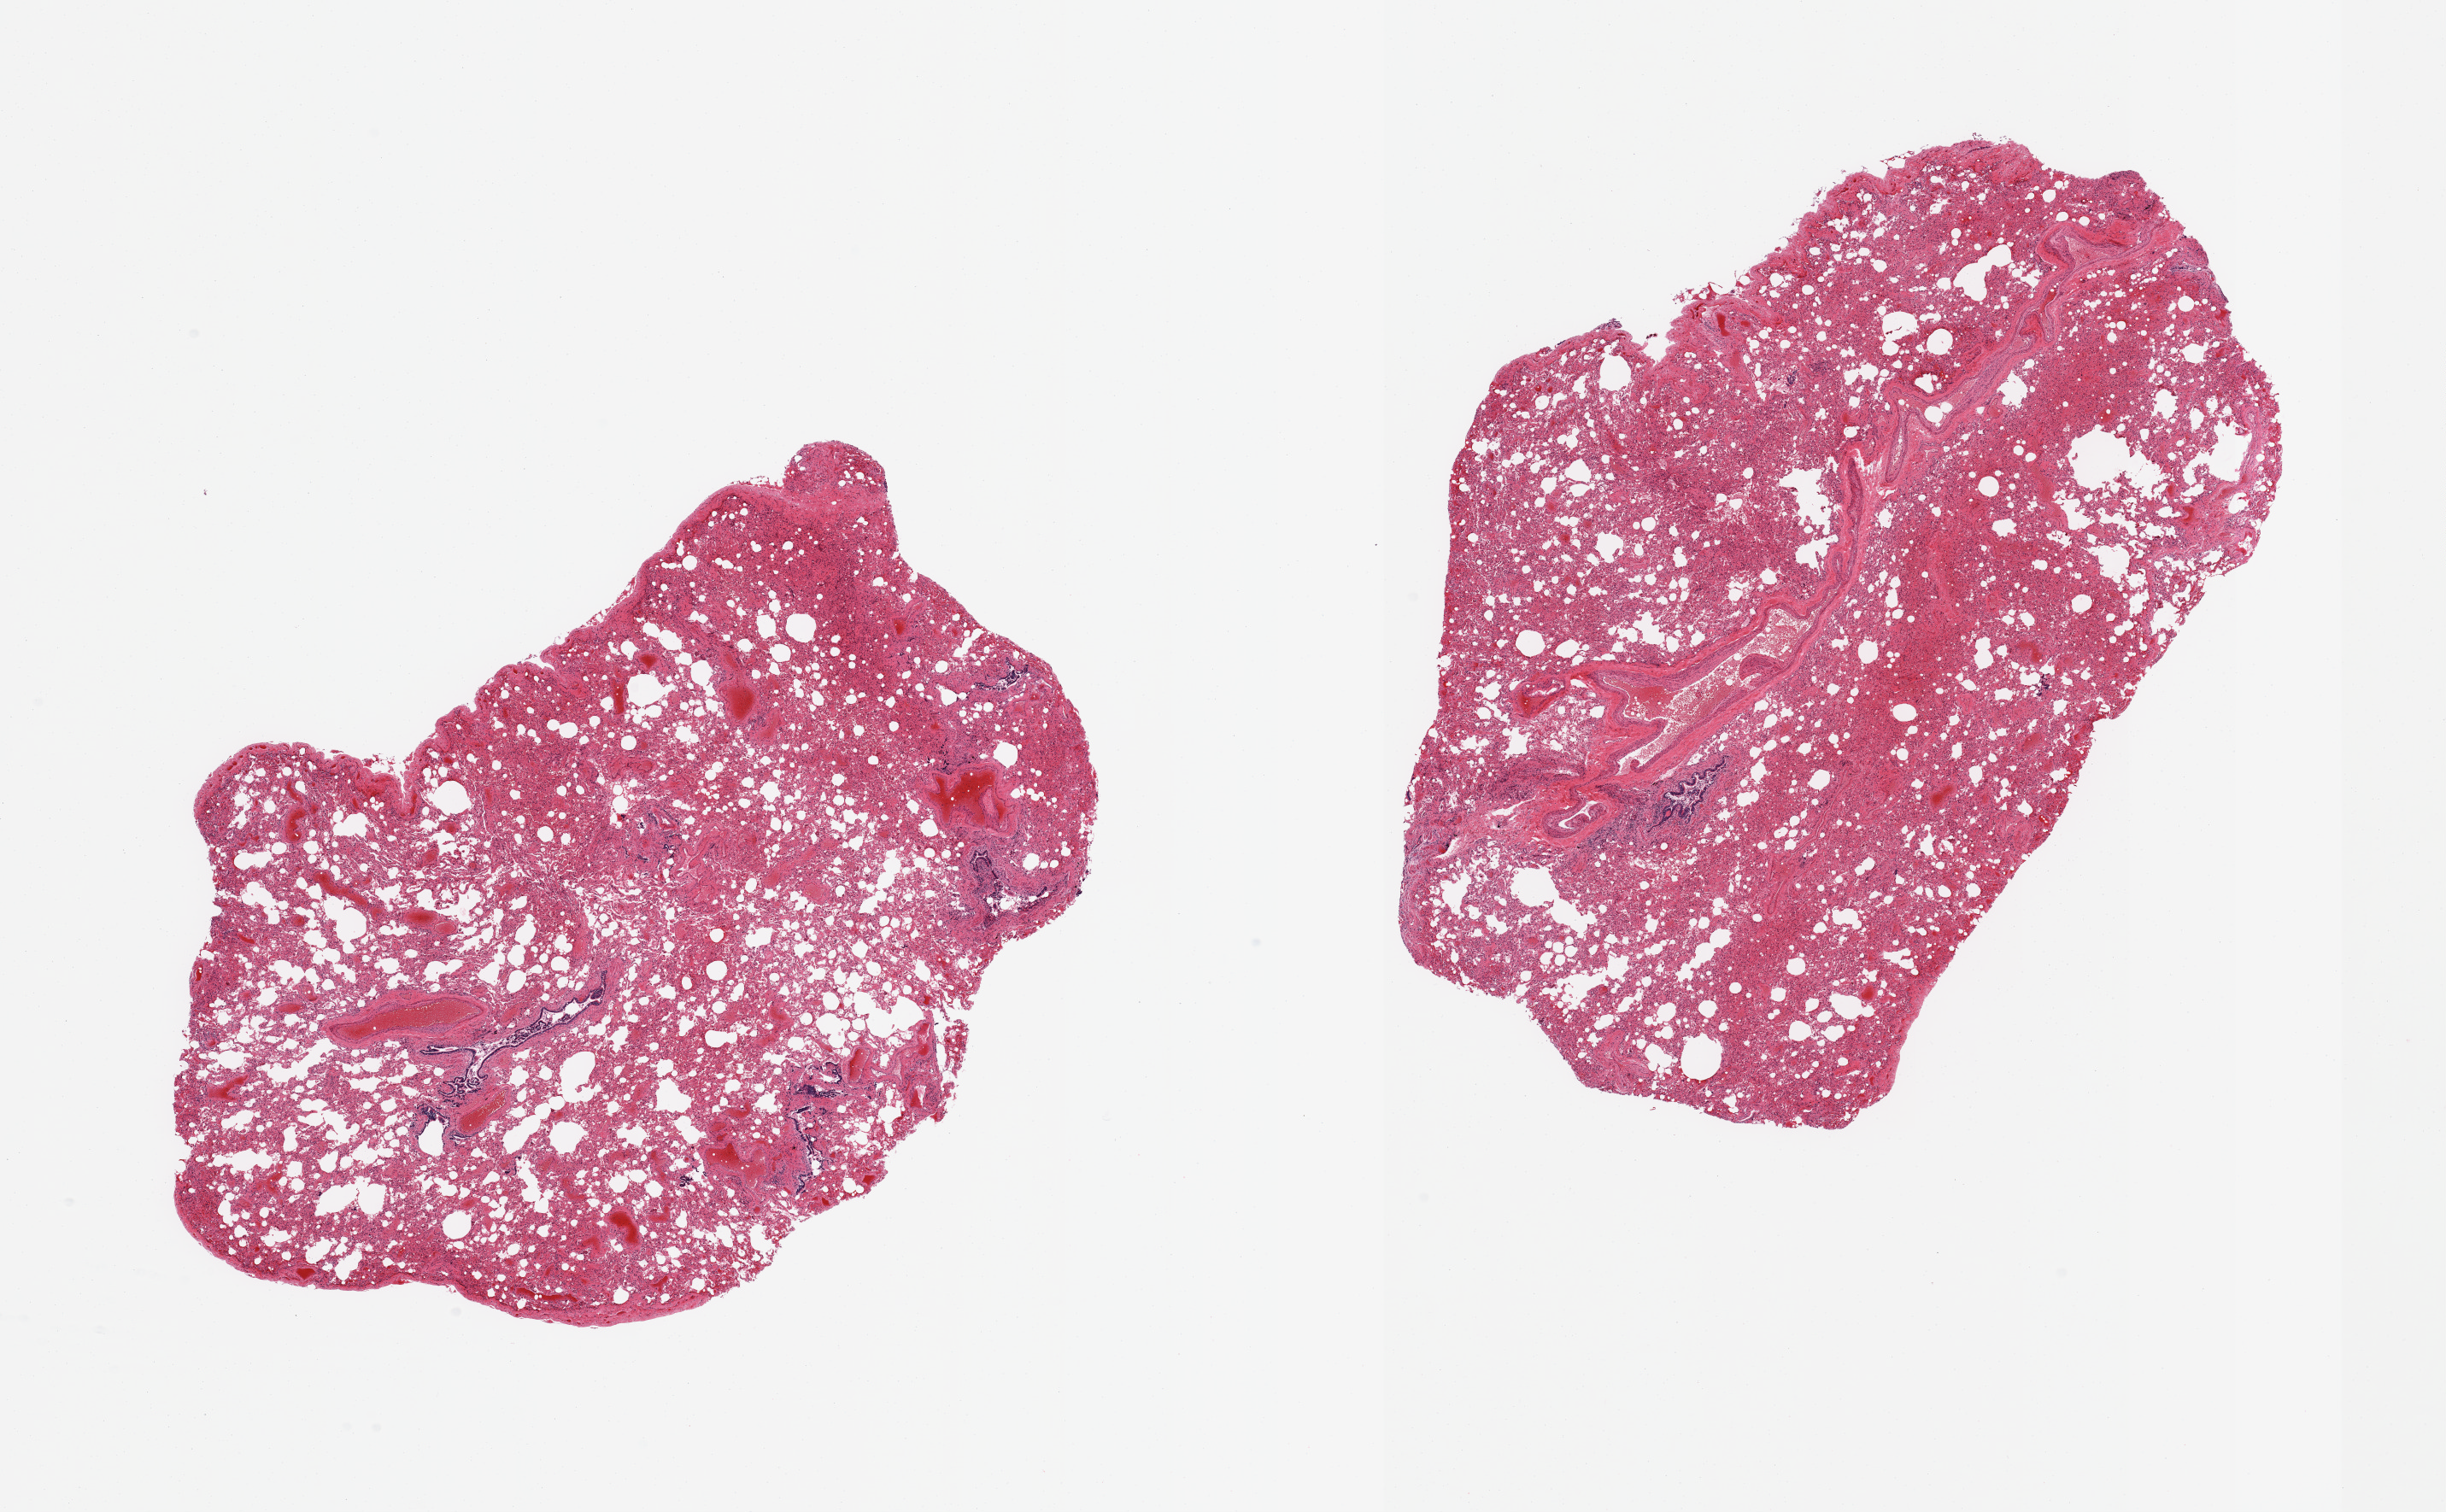
Whole-slide image, hematoxylin and eosin (H&E) stain, low-resolution overview of the scanned area, about 22.6 x 14.0 mm, PAXgene-fixed, paraffin-embedded tissue, sampled site (target tissue): lung, donor tissue sample. Male donor.
Review note (as recorded): 2 pieces, moderate congestion.